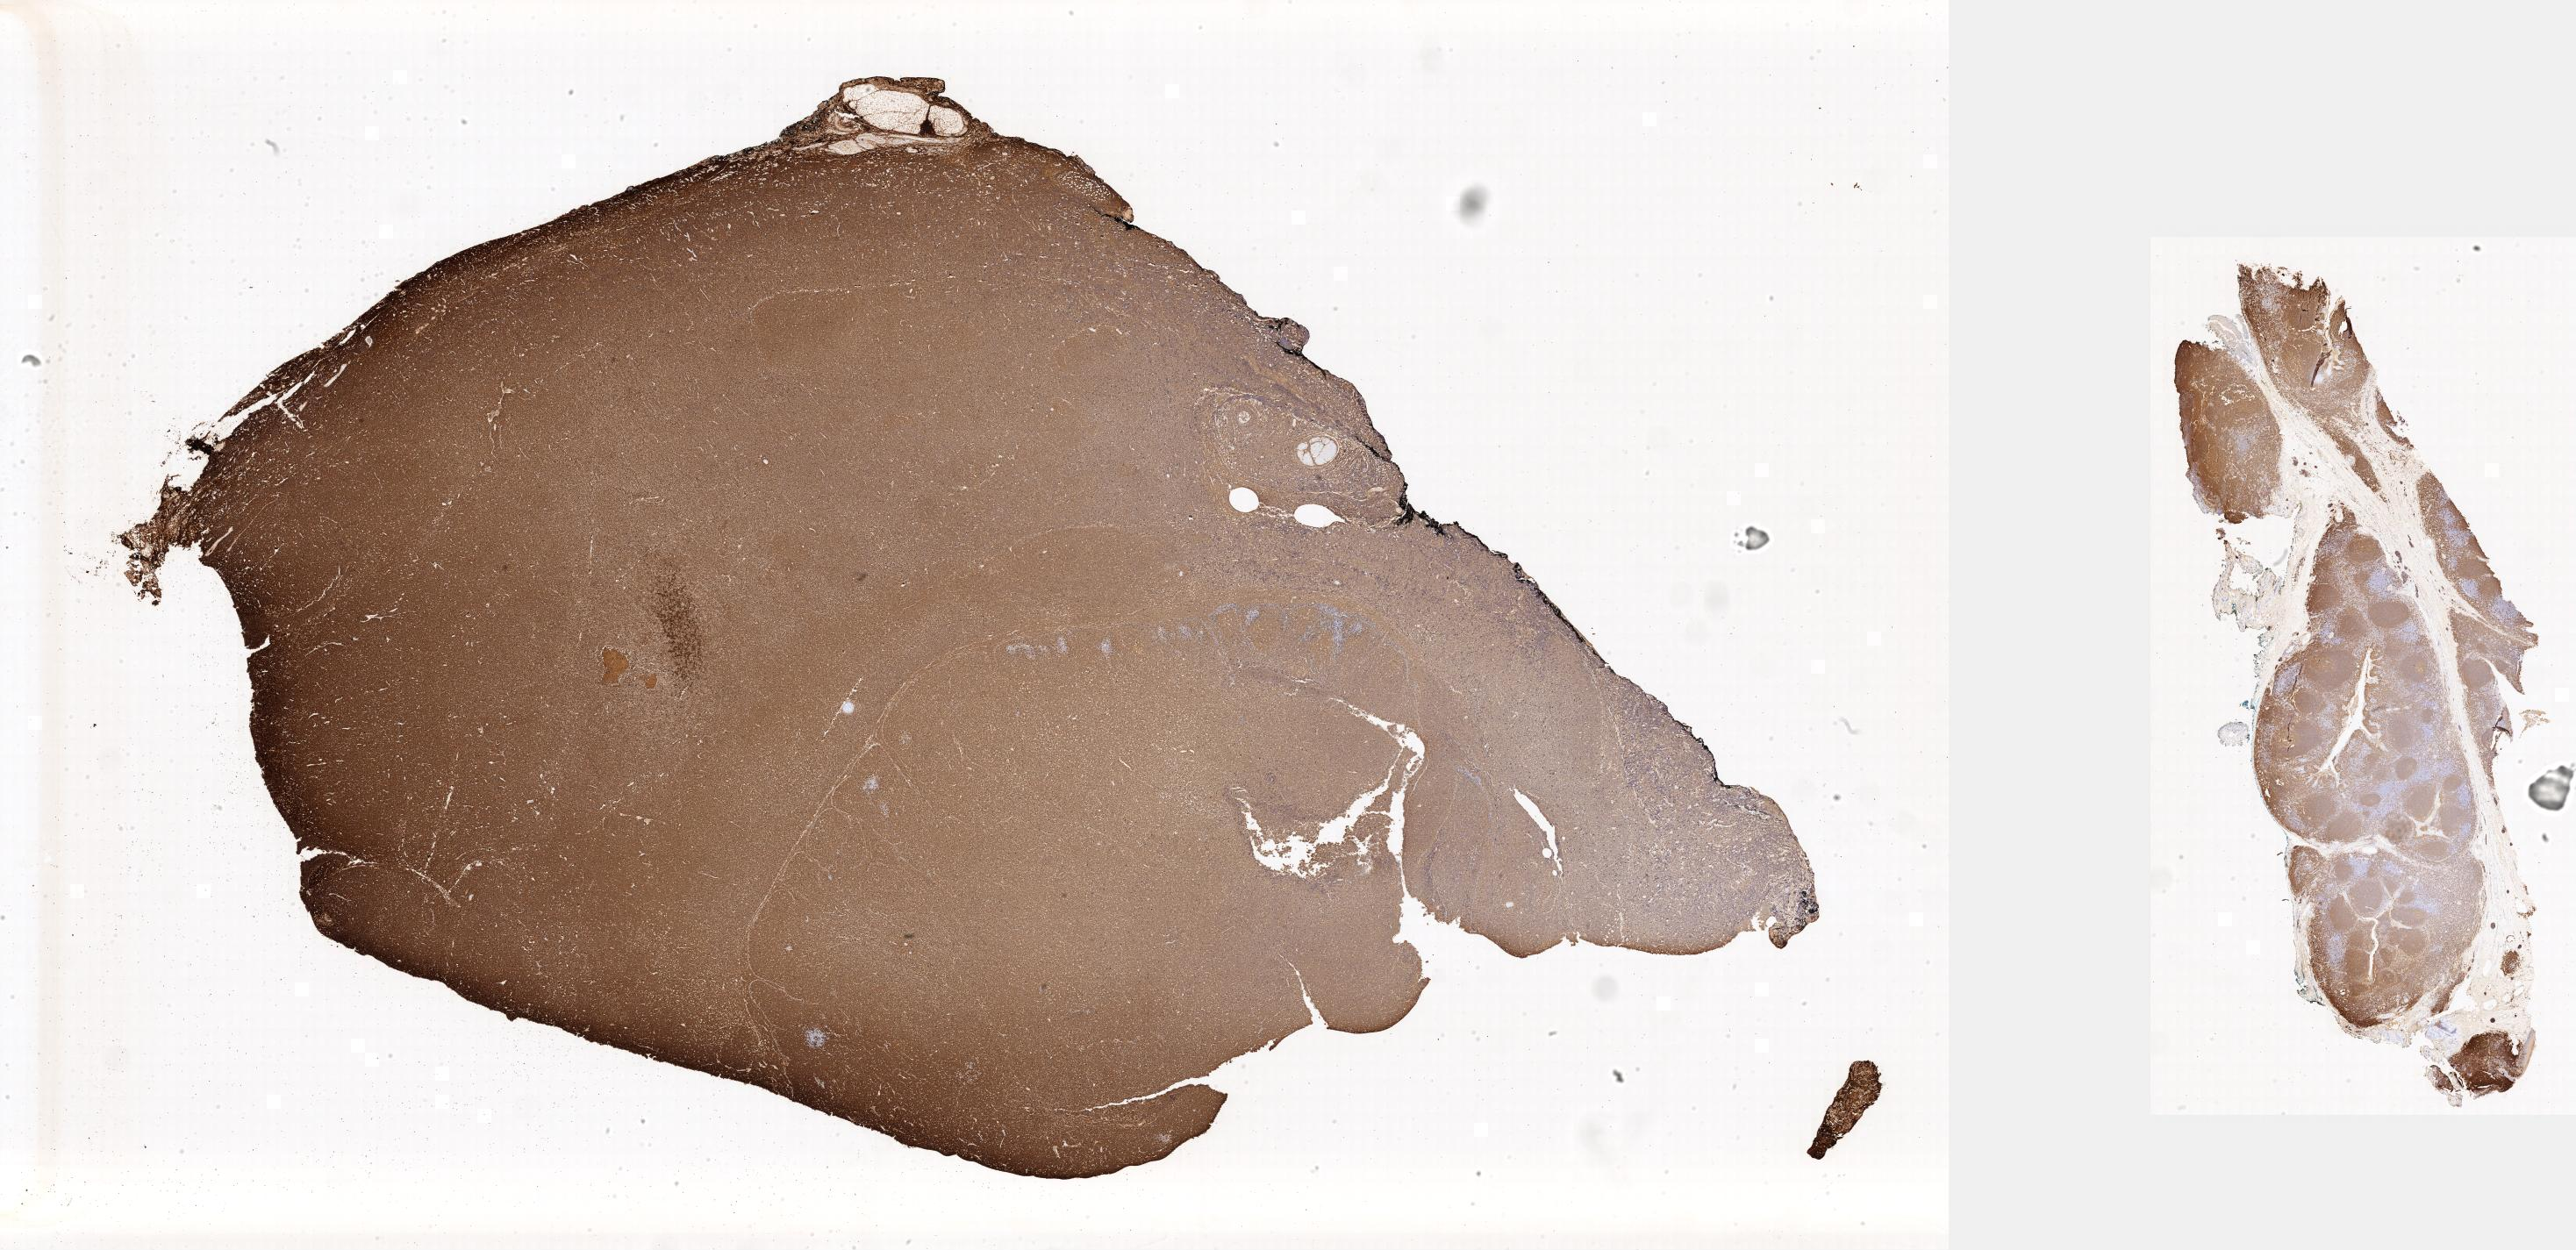
Immunohistochemistry (IHC) whole-slide image stained for CD20 — low-resolution overview of the scanned area; specimen: tumor tissue; site: lymph node of head and neck. Male patient; age at initial diagnosis 6 years.
Diagnosis: Burkitt lymphoma, NOS.